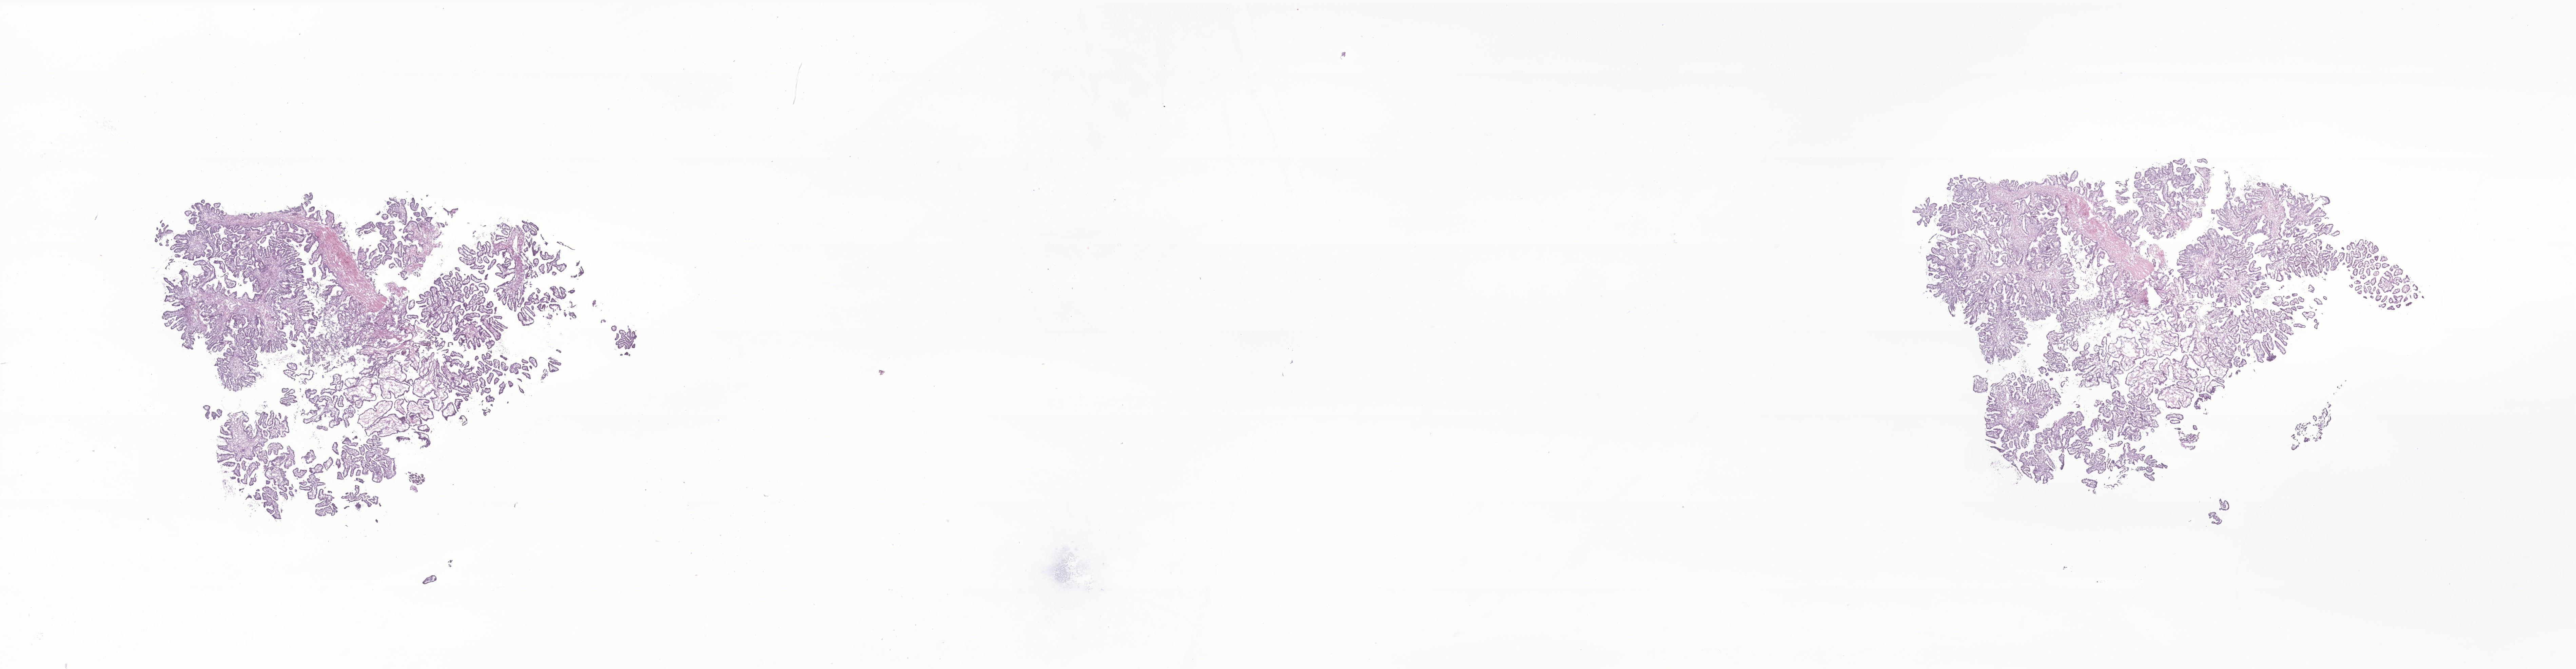
H&E whole-slide image of tumor tissue from the brain, whole scanned area (about 32.0 x 8.3 mm) shown as a low-resolution overview, frozen section (OCT-embedded). Male patient, age 201 months.
• recorded diagnosis: Choroid plexus papilloma, NOS